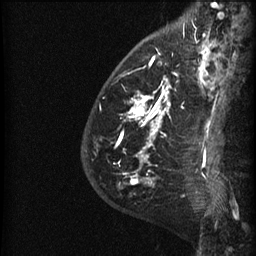
Breast MRI (dynamic contrast-enhanced), one sagittal slice; slice 13 of 60 in the series (ordered by position); dynamic contrast-enhanced series, image 2 of 3 at this slice position (ordered by acquisition); 1.5 T; TE 4.2 ms, TR 22.7 ms; 1.5 mm slice thickness; 256 × 256 image matrix, field of view 180 × 180 mm. Patient: female, 48 years. Case-level facts recorded for this patient, not image findings: setting: breast cancer imaged before/during neoadjuvant chemotherapy; receptor status: triple-negative.
Structures marked on this image (semi-automatic segmentation, software-assisted and operator-edited):
- analysis volume of interest (the breast-tissue region the enhancement analysis was run in; not a lesion): bounding box [x1, y1, x2, y2] px = [89, 27, 191, 180]
- tumour enhancement mask (voxels above the 90 % enhancement threshold inside the analysis volume of interest): [119, 56, 175, 180]